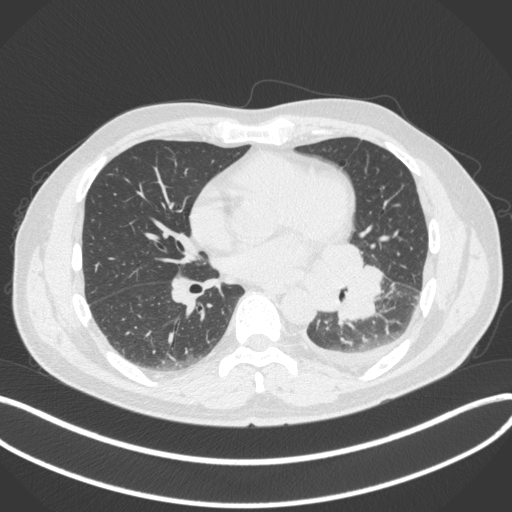
Chest CT, one axial slice. Position 166 of 350 along the scan axis. Reconstruction kernel B31f. Lung window (W 1500 / L -600 HU). 1 mm slice thickness. 512 × 512 image matrix, field of view 400 × 400 mm. Male patient, age 58 years. Case-level facts recorded for this patient, not image findings: clinical TNM (as recorded): T3 N1 M1b; histopathological grade: G3.
Structures marked on this image (rectangle marked by the reading radiologist):
- lung tumour (recorded histology: small cell carcinoma): box from (x=308, y=239) to (x=383, y=324) px